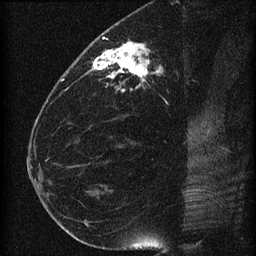
Breast MRI (dynamic contrast-enhanced), one sagittal slice. Position 30 of 60 along the scan axis. Dynamic contrast-enhanced series, image 2 of 4 at this slice position (ordered by acquisition). 1.5 T. TE 4.2 ms, TR 22.7 ms. 256 × 256 image matrix, field of view 180 × 180 mm. Patient: female, 35 years. Case-level facts recorded for this patient, not image findings: setting: breast cancer imaged before/during neoadjuvant chemotherapy; receptor status: HR-positive, HER2-negative.
Structures marked on this image (semi-automatically segmented with operator editing):
- analysis volume of interest (the breast-tissue region the enhancement analysis was run in; not a lesion): bounding box (x1, y1, x2, y2) in pixels: (69, 27, 197, 110)
- tumour enhancement mask (voxels above the 90 % enhancement threshold inside the analysis volume of interest): (92, 37, 160, 91)